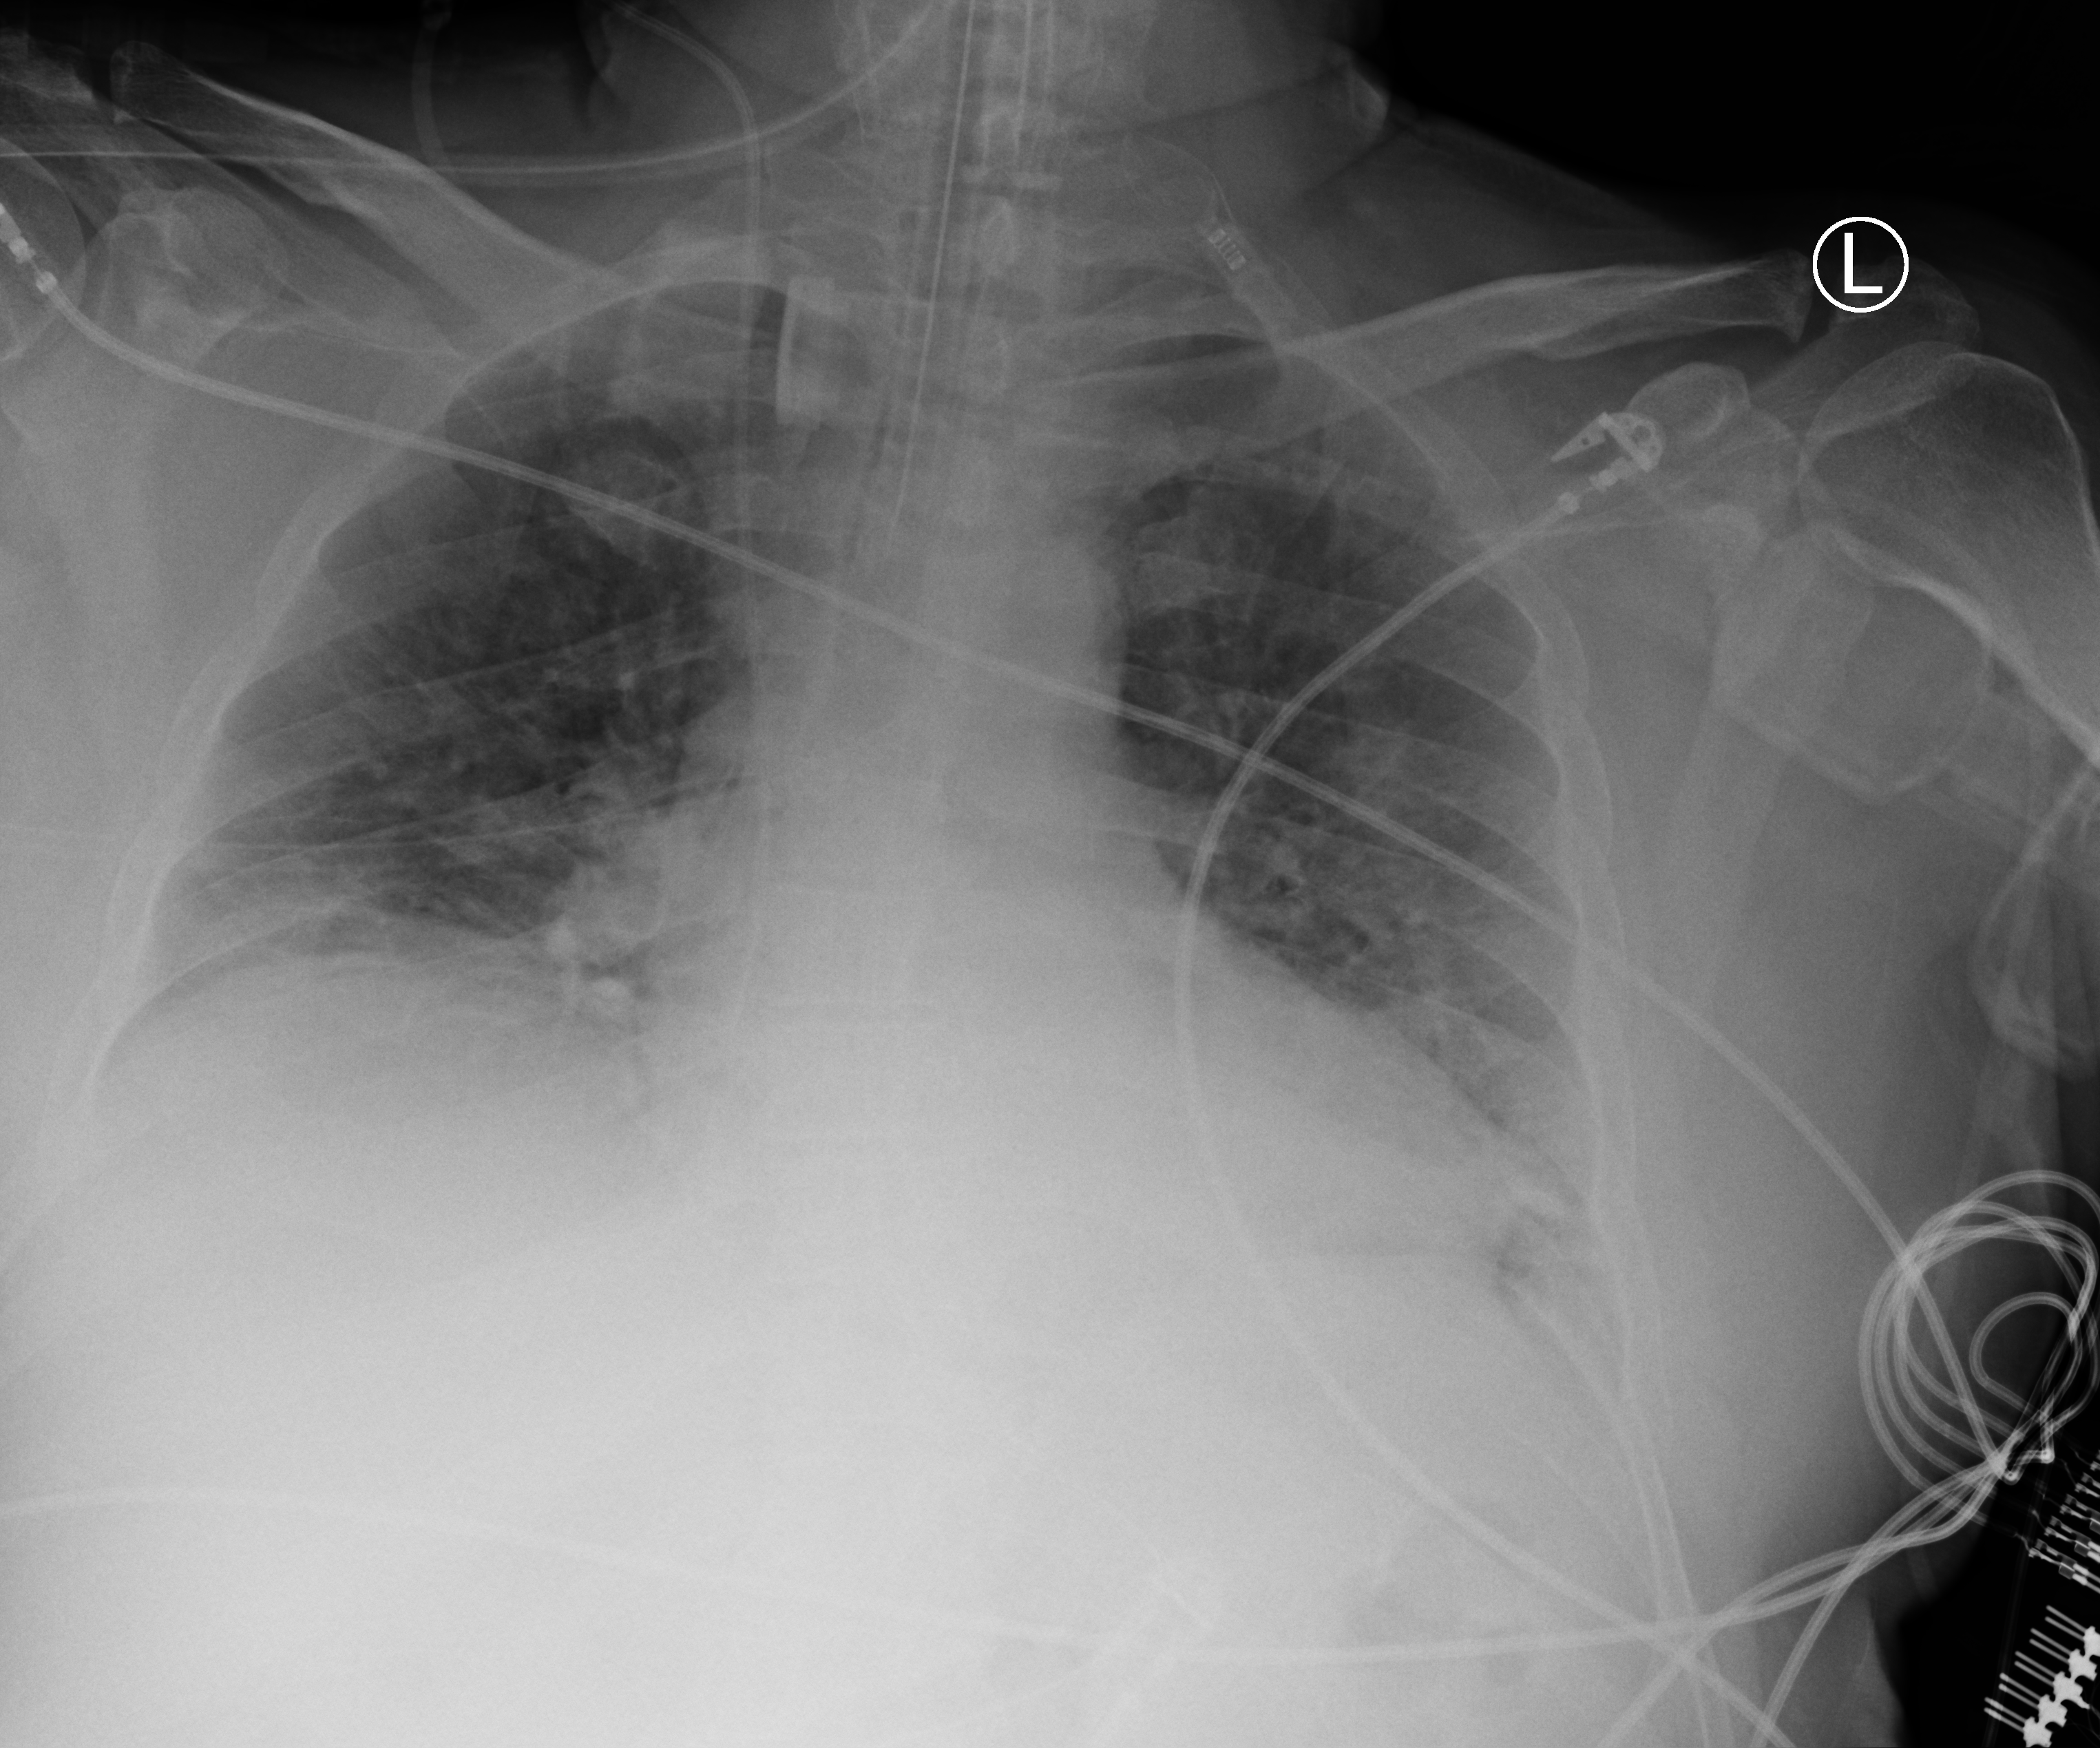
Portable chest radiograph; anteroposterior (AP) projection. Male patient hospitalised with COVID-19, age 18–59 years.
Hospital-stay facts (about this admission, not read from this image; timing relative to this image not recorded): smoking status (admission record): never; diabetes (admission record): yes.